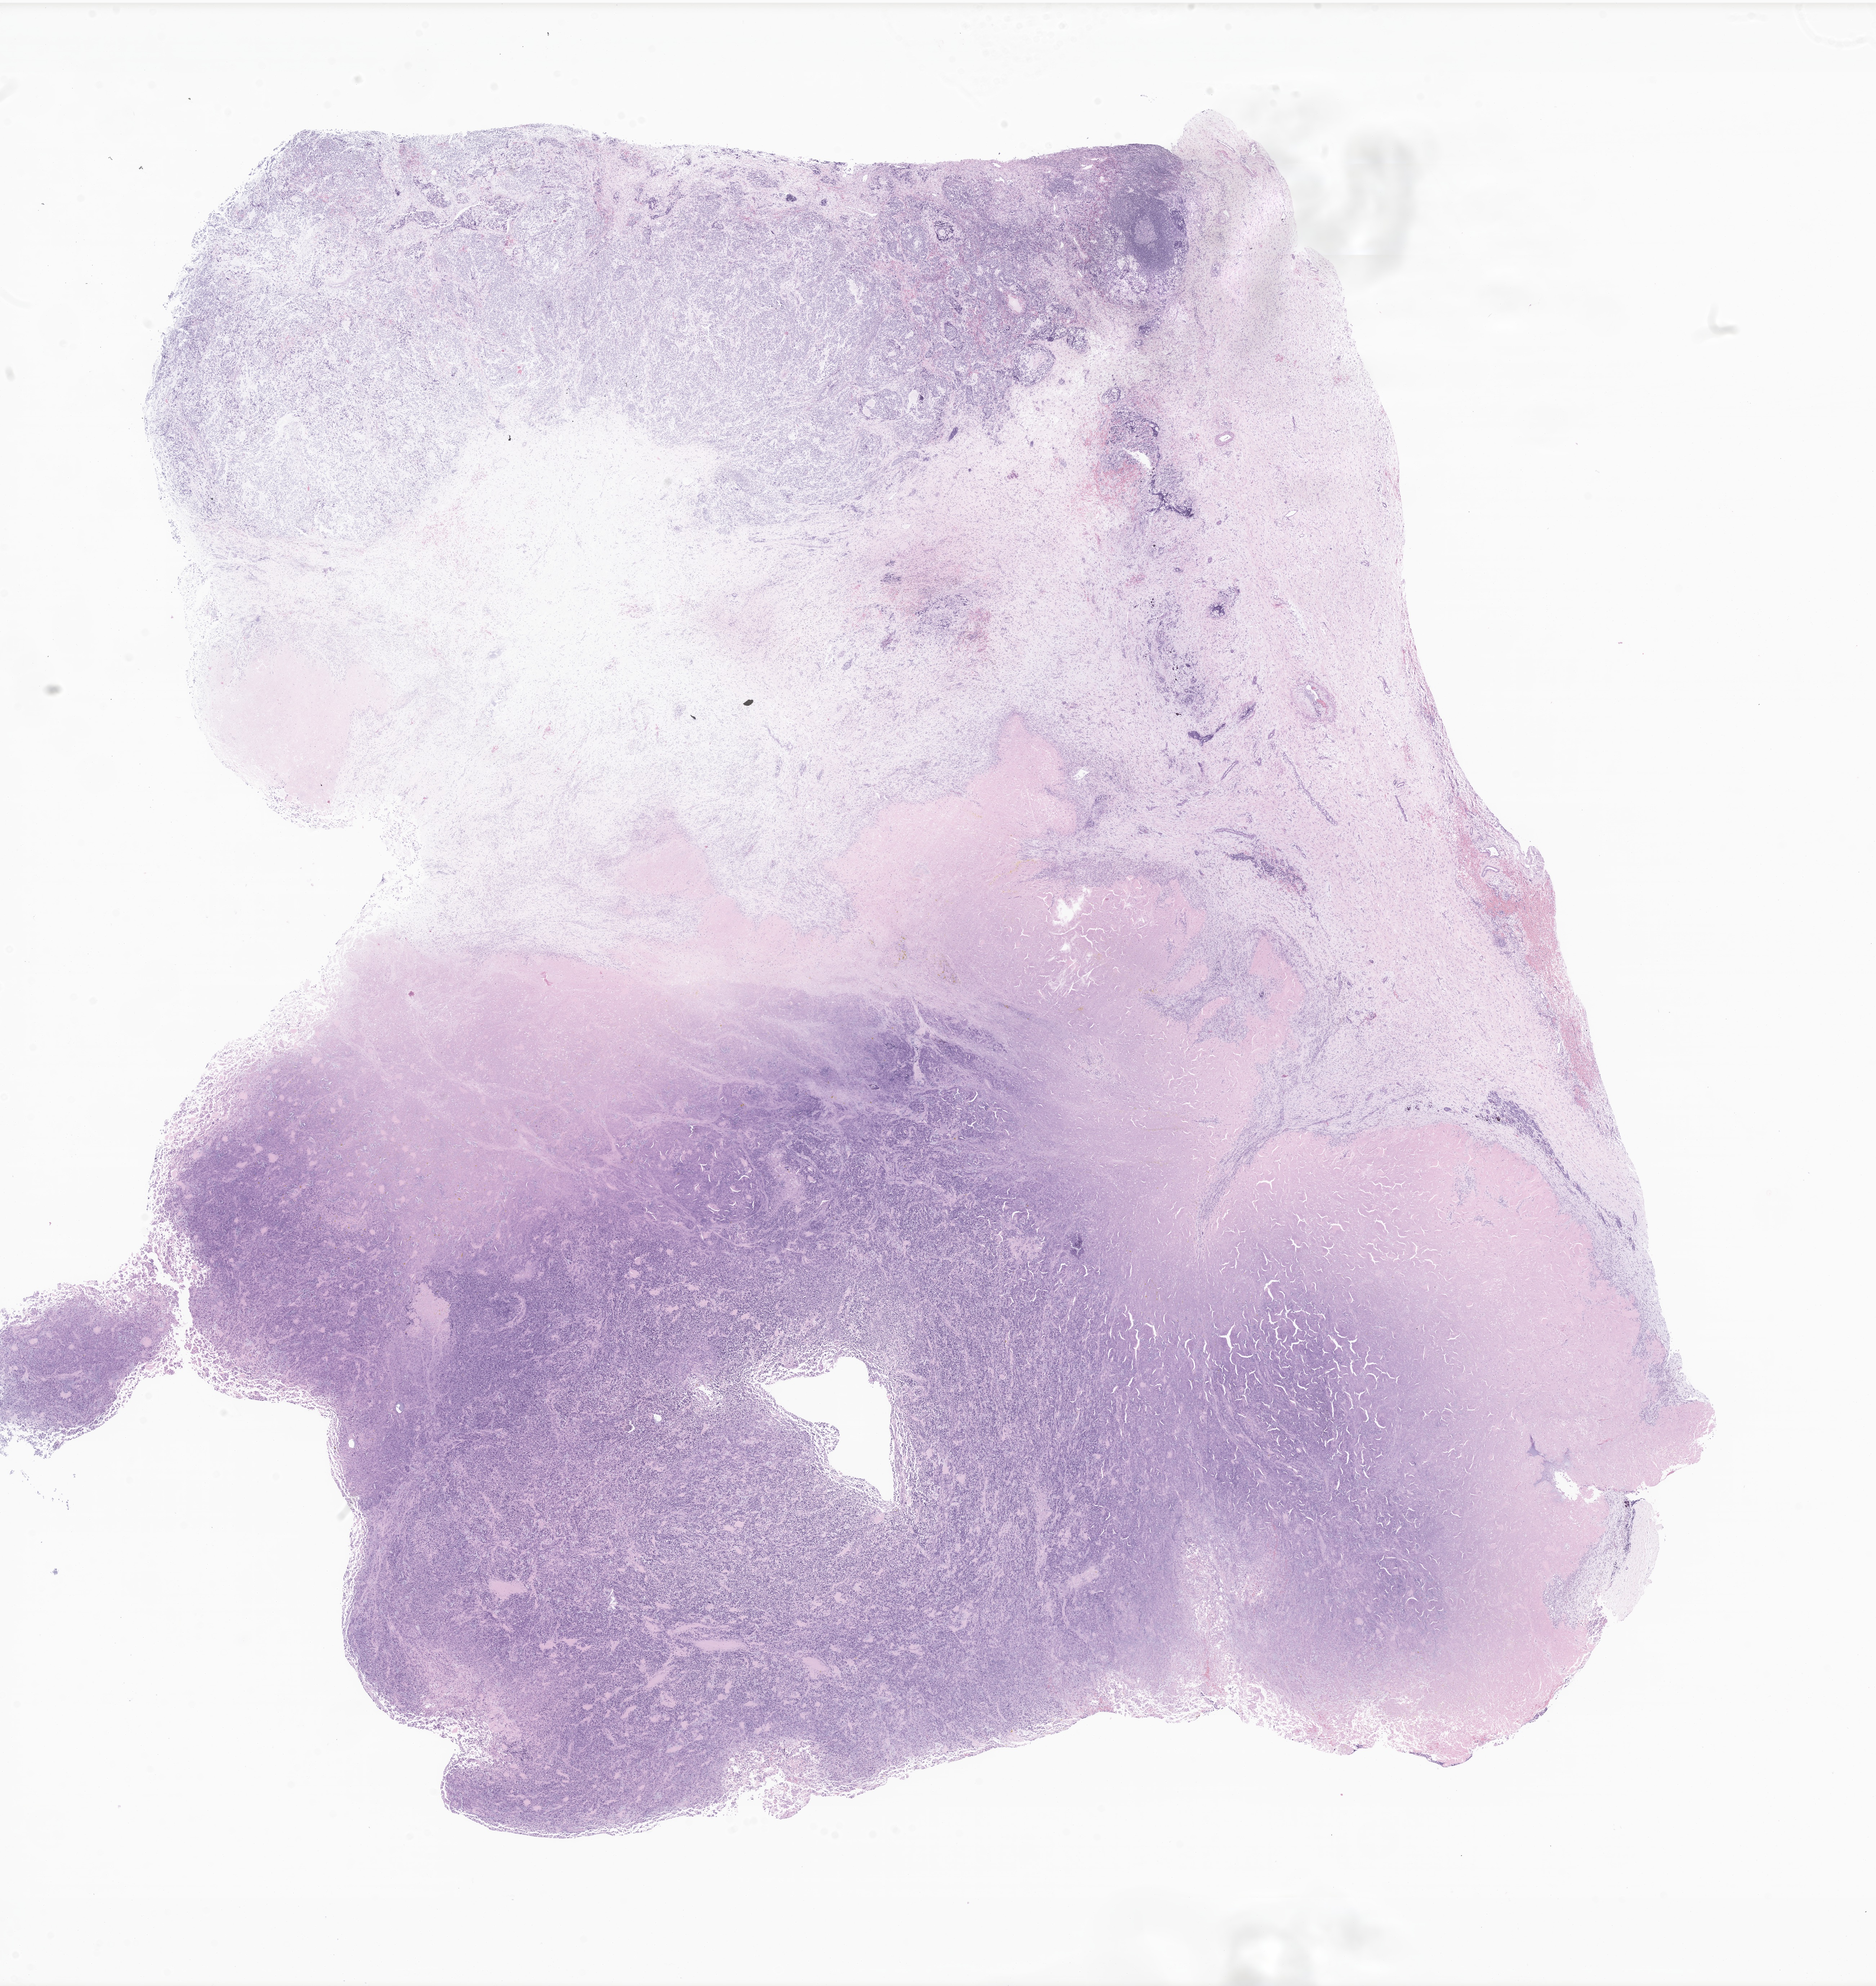
Haematoxylin and eosin whole-slide image of tumor tissue from the retroperitoneum, whole scanned area (about 22.0 x 23.2 mm) shown as a low-resolution overview; FFPE section. Female patient, age 68 months.
* diagnosis (ICD-O-3 morphology term): Neuroblastoma, NOS